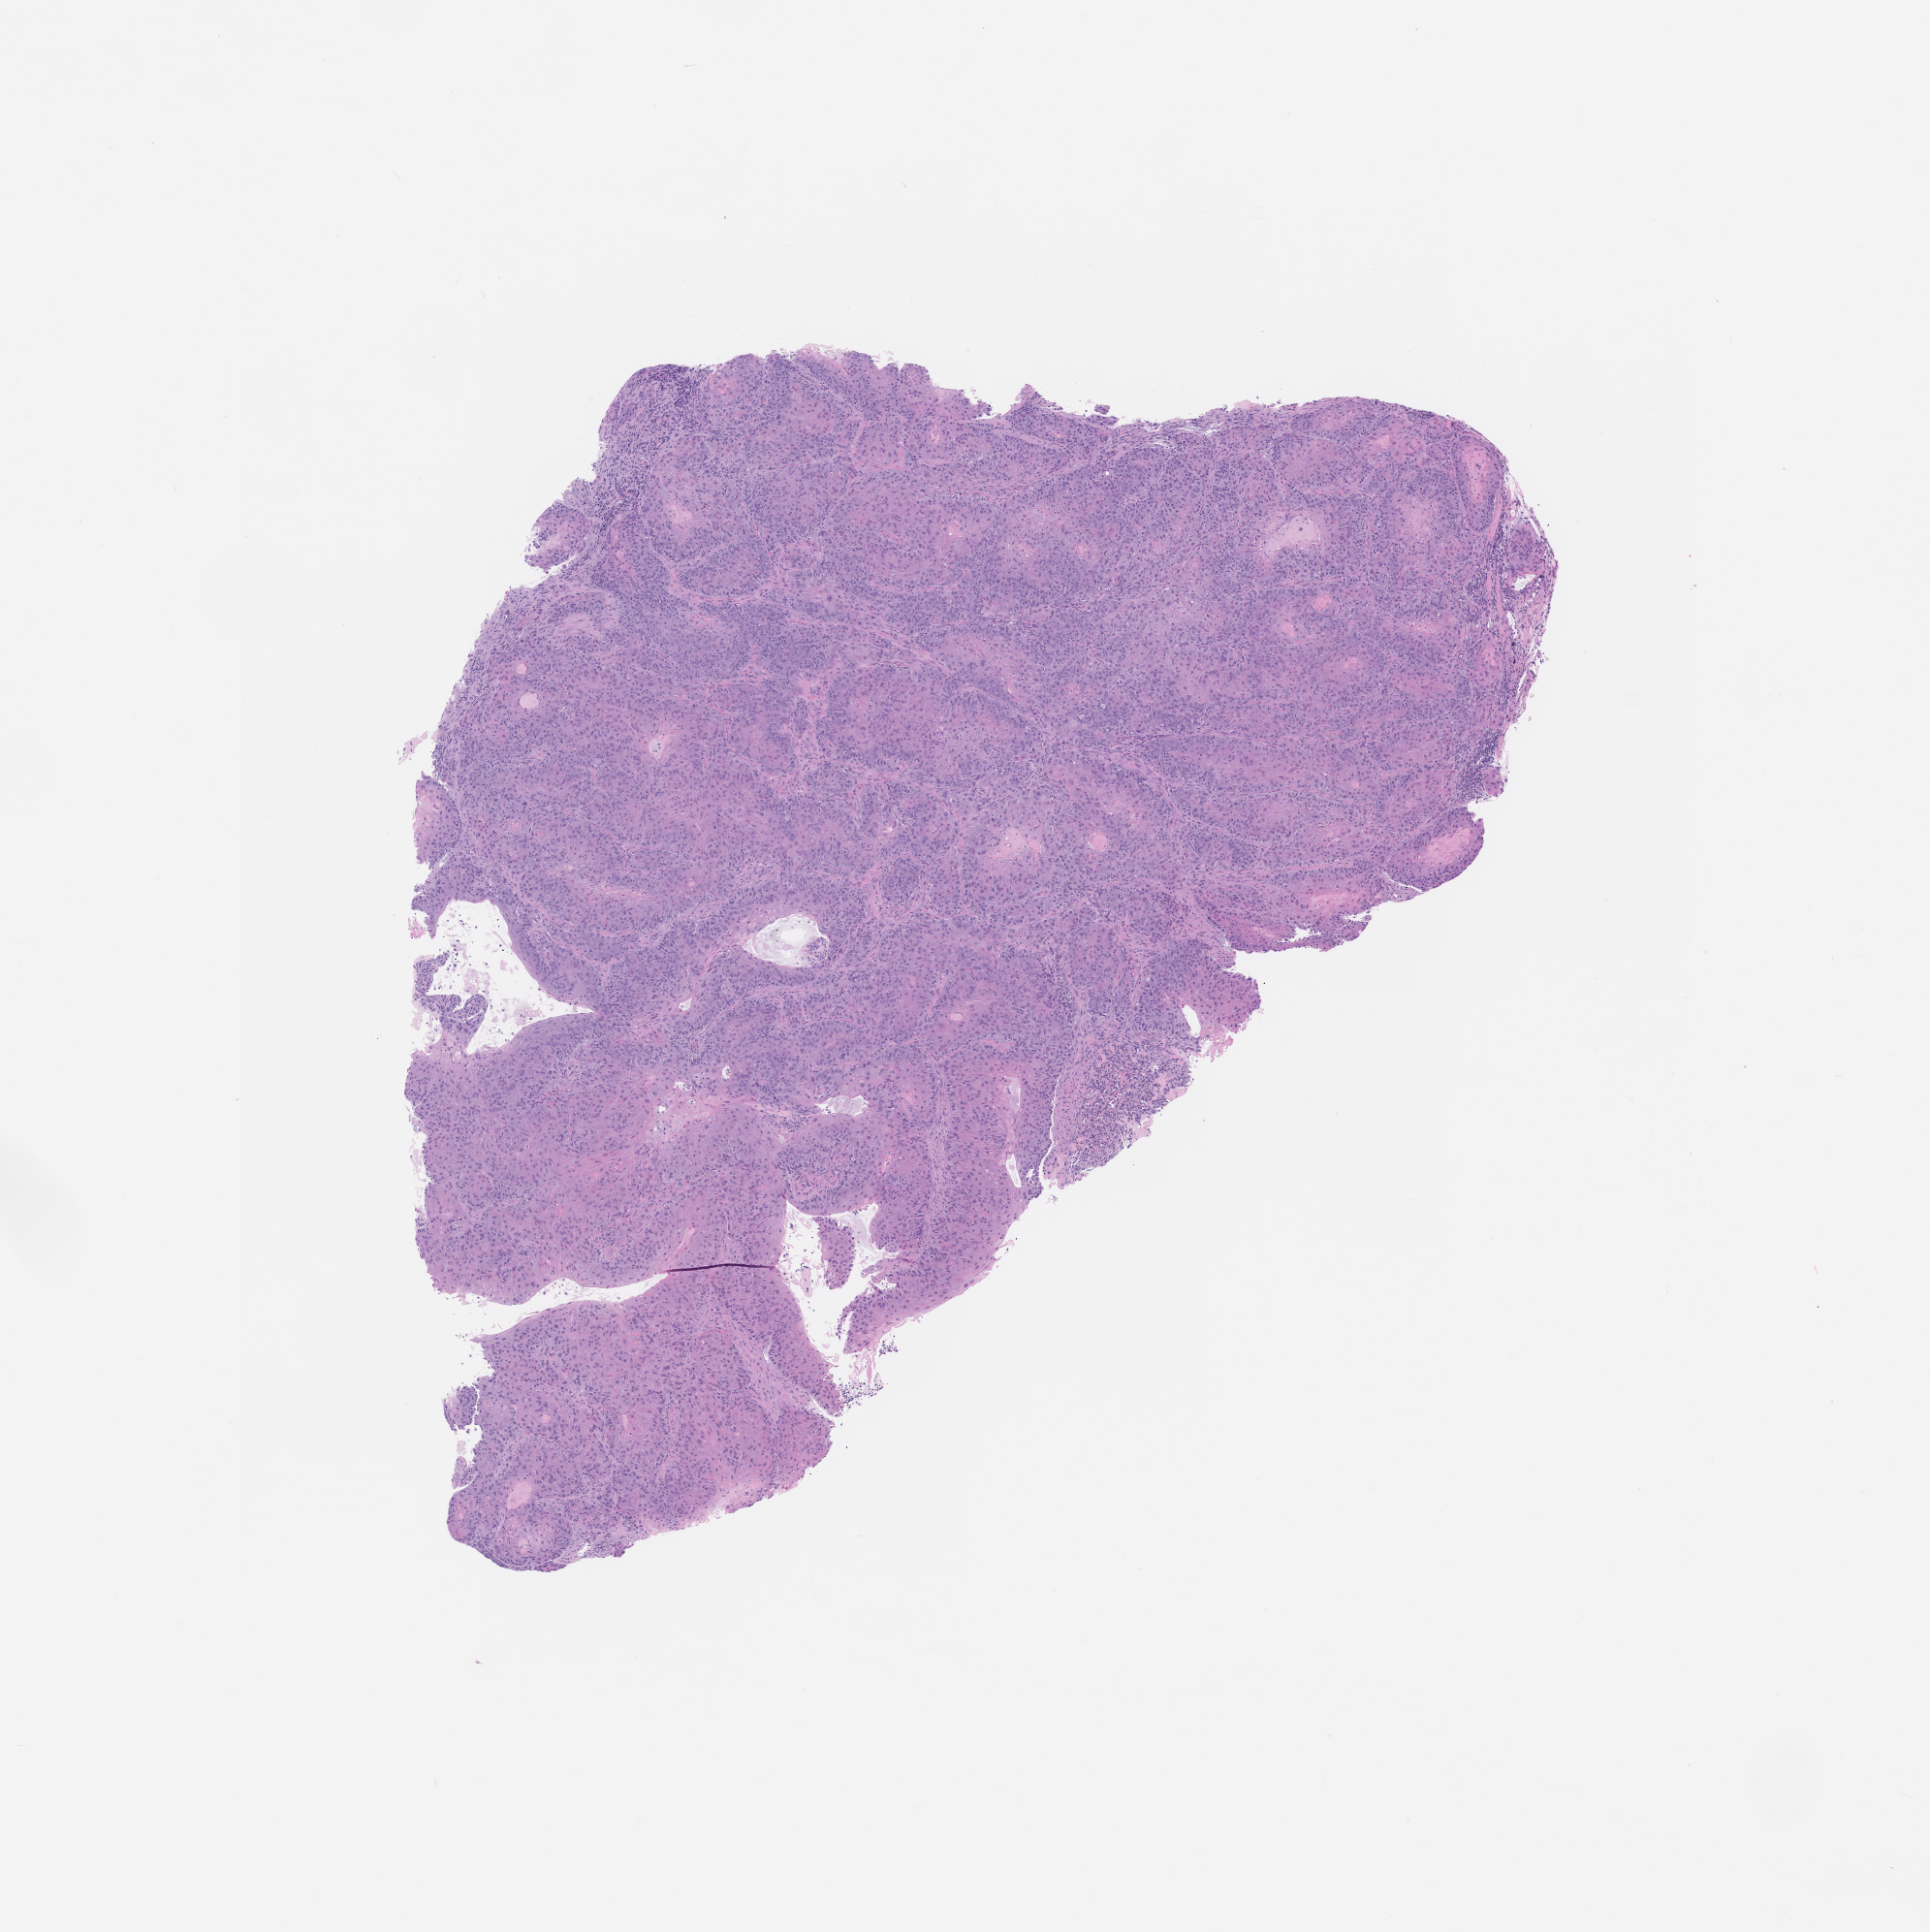
Whole-slide image, hematoxylin and eosin (H&E): patient-derived xenograft (human tumor grown in a mouse), passage 0 — a low-resolution overview of the entire scanned area, about 8.0 x 8.0 mm. Formalin-fixed paraffin-embedded section. Originating tumor site category: lung.
• originating patient diagnosis: Lung Squamous Cell Carcinoma